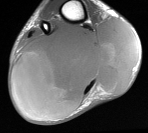
MRI of an extremity soft-tissue mass, one axial slice. Position 28 of 76 along the scan axis. MR volume resampled by the dataset authors to the PET/CT grid (not the native acquisition matrix). 3.27 mm slice thickness. 148 × 133 image matrix, field of view 145 × 130 mm. Male patient. From the clinical record (not read from this slice): histological type: liposarcoma - round cell; grade: high; site of the primary tumour: right calf.
Annotated regions visible in this slice (expert contour drawn on MRI and transferred to this co-registered scan by the dataset authors):
- gross tumour volume (mass): bounding box [x1, y1, x2, y2] px = [13, 17, 139, 116]